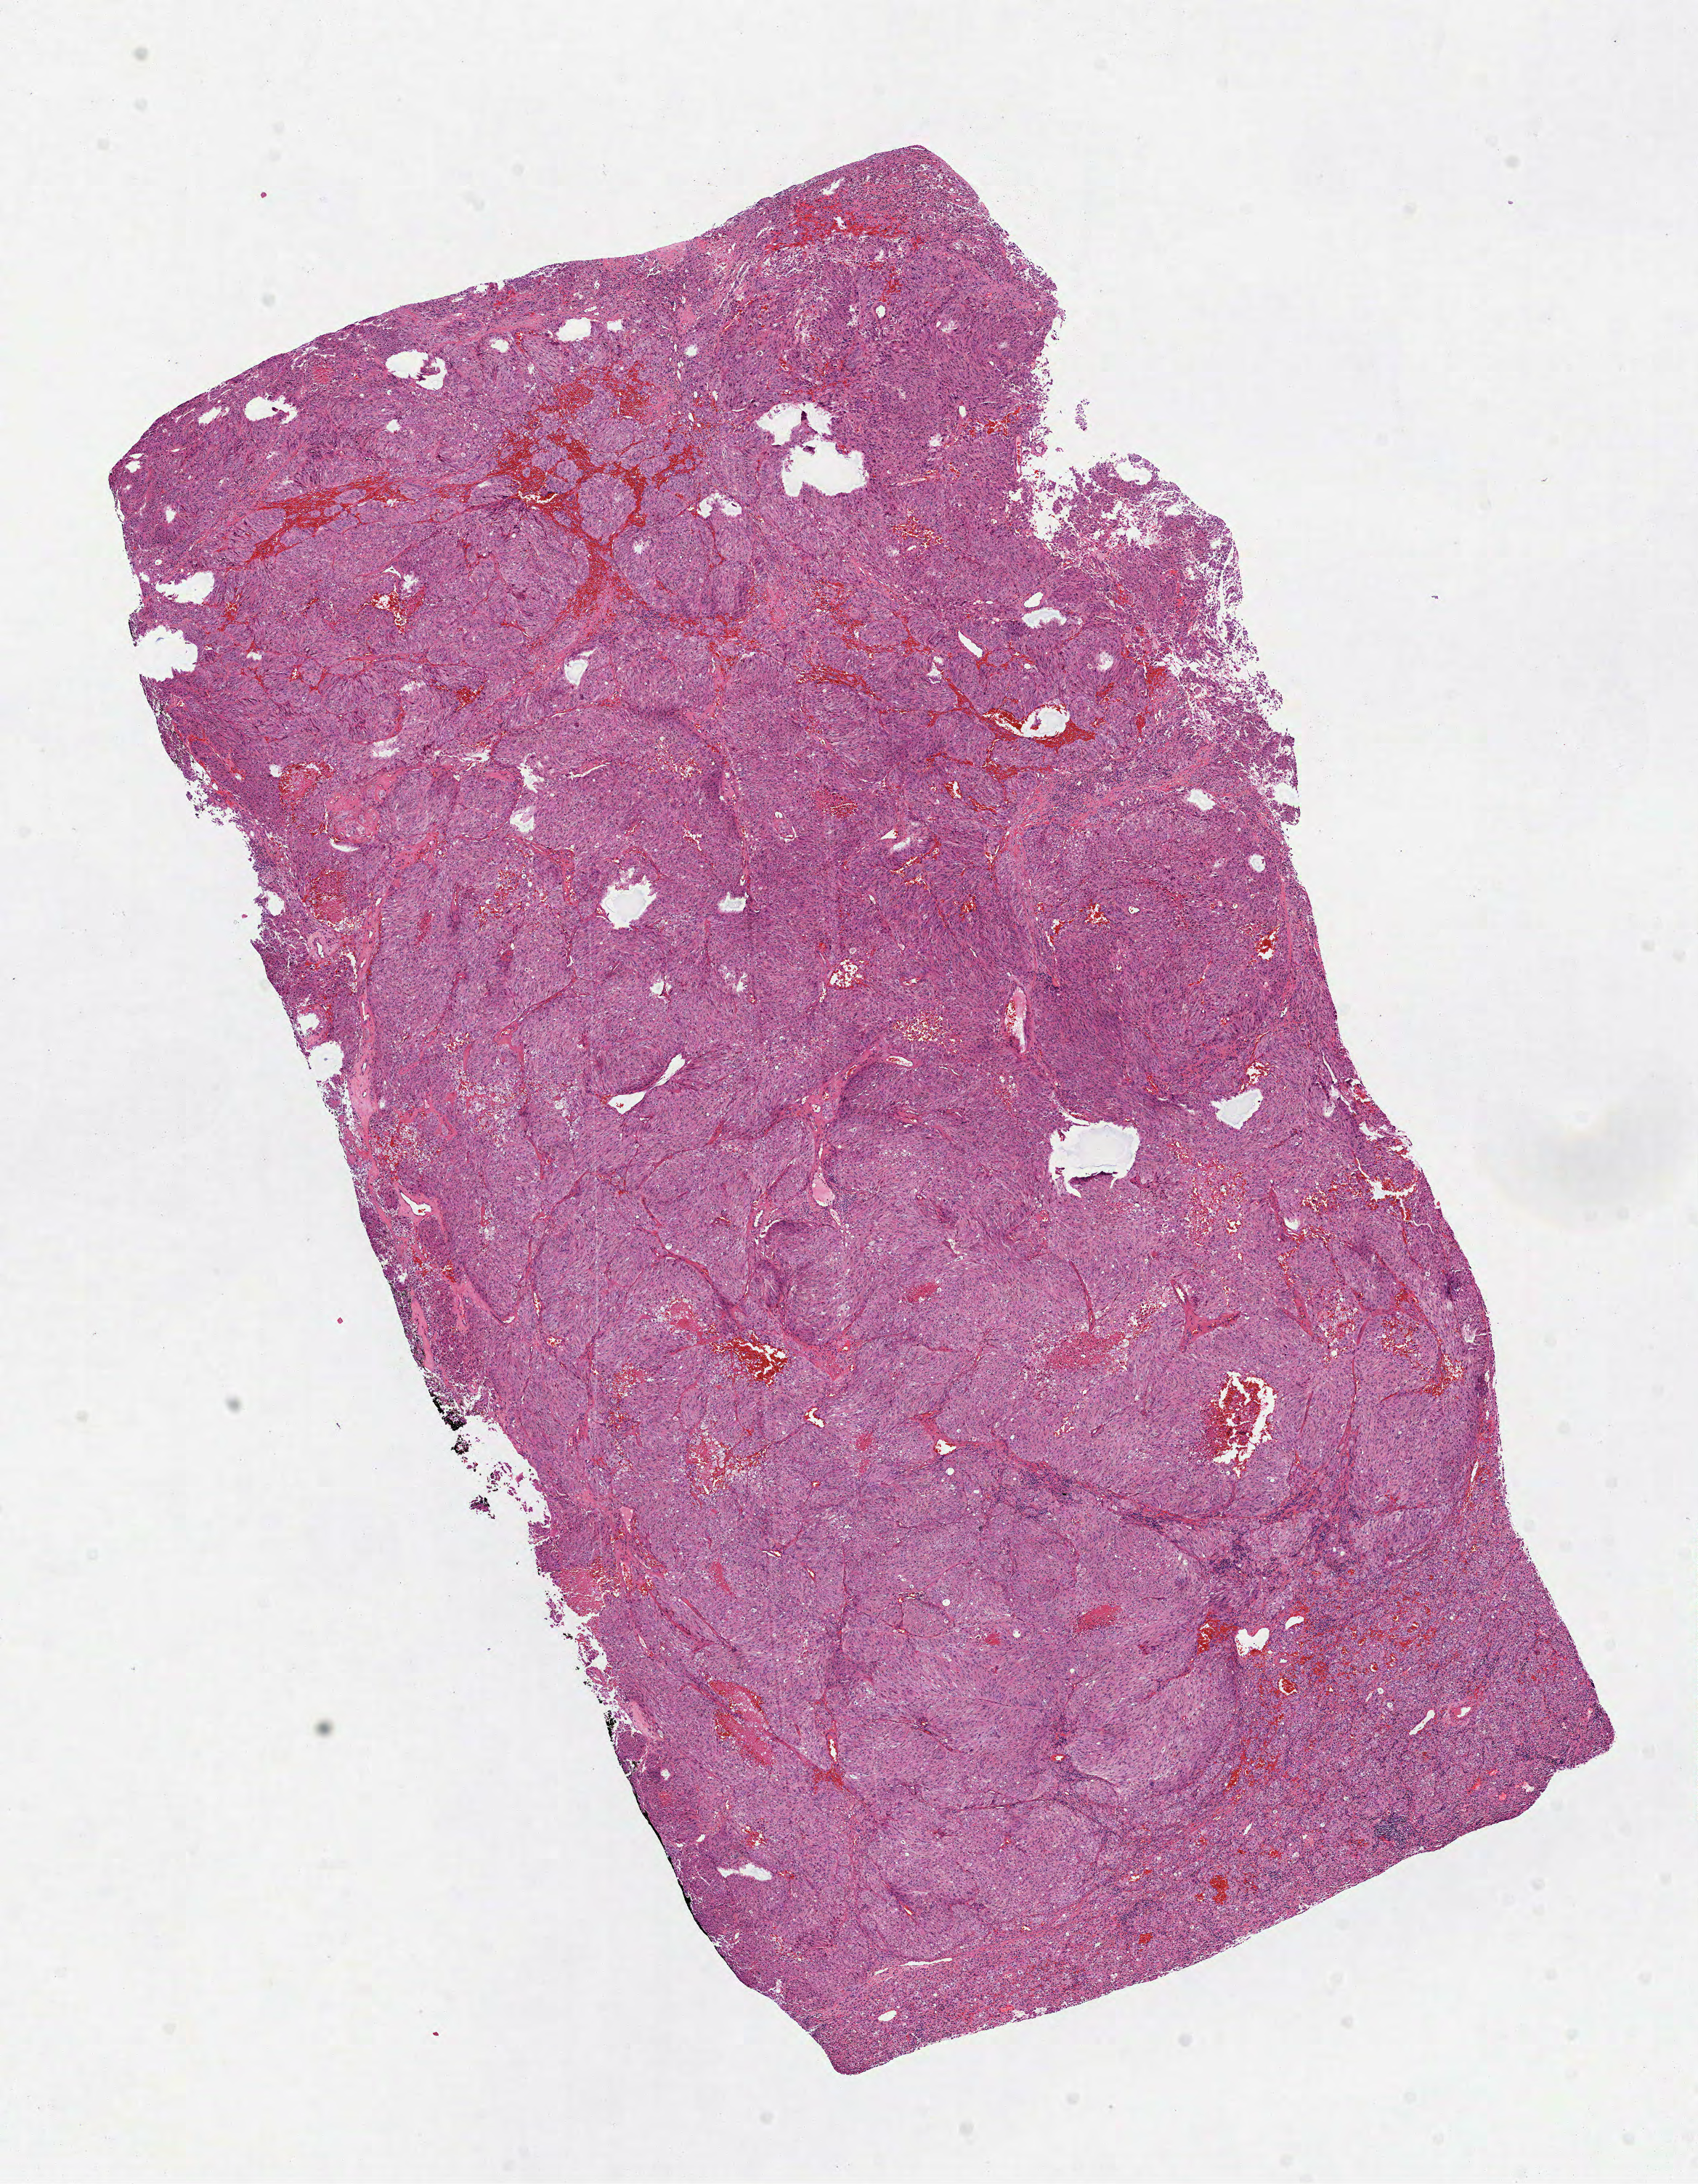
Hematoxylin and eosin (H&E) stained whole-slide image, low-resolution overview of the scanned area, about 9.4 x 12.1 mm (acquisition: 40x scan), formalin-fixed paraffin-embedded (FFPE) diagnostic section, skin, primary tumour sample. Female, age 57 years at initial diagnosis.
Diagnosis: Malignant melanoma, NOS. AJCC pathologic stage: IIIB (7th edition).